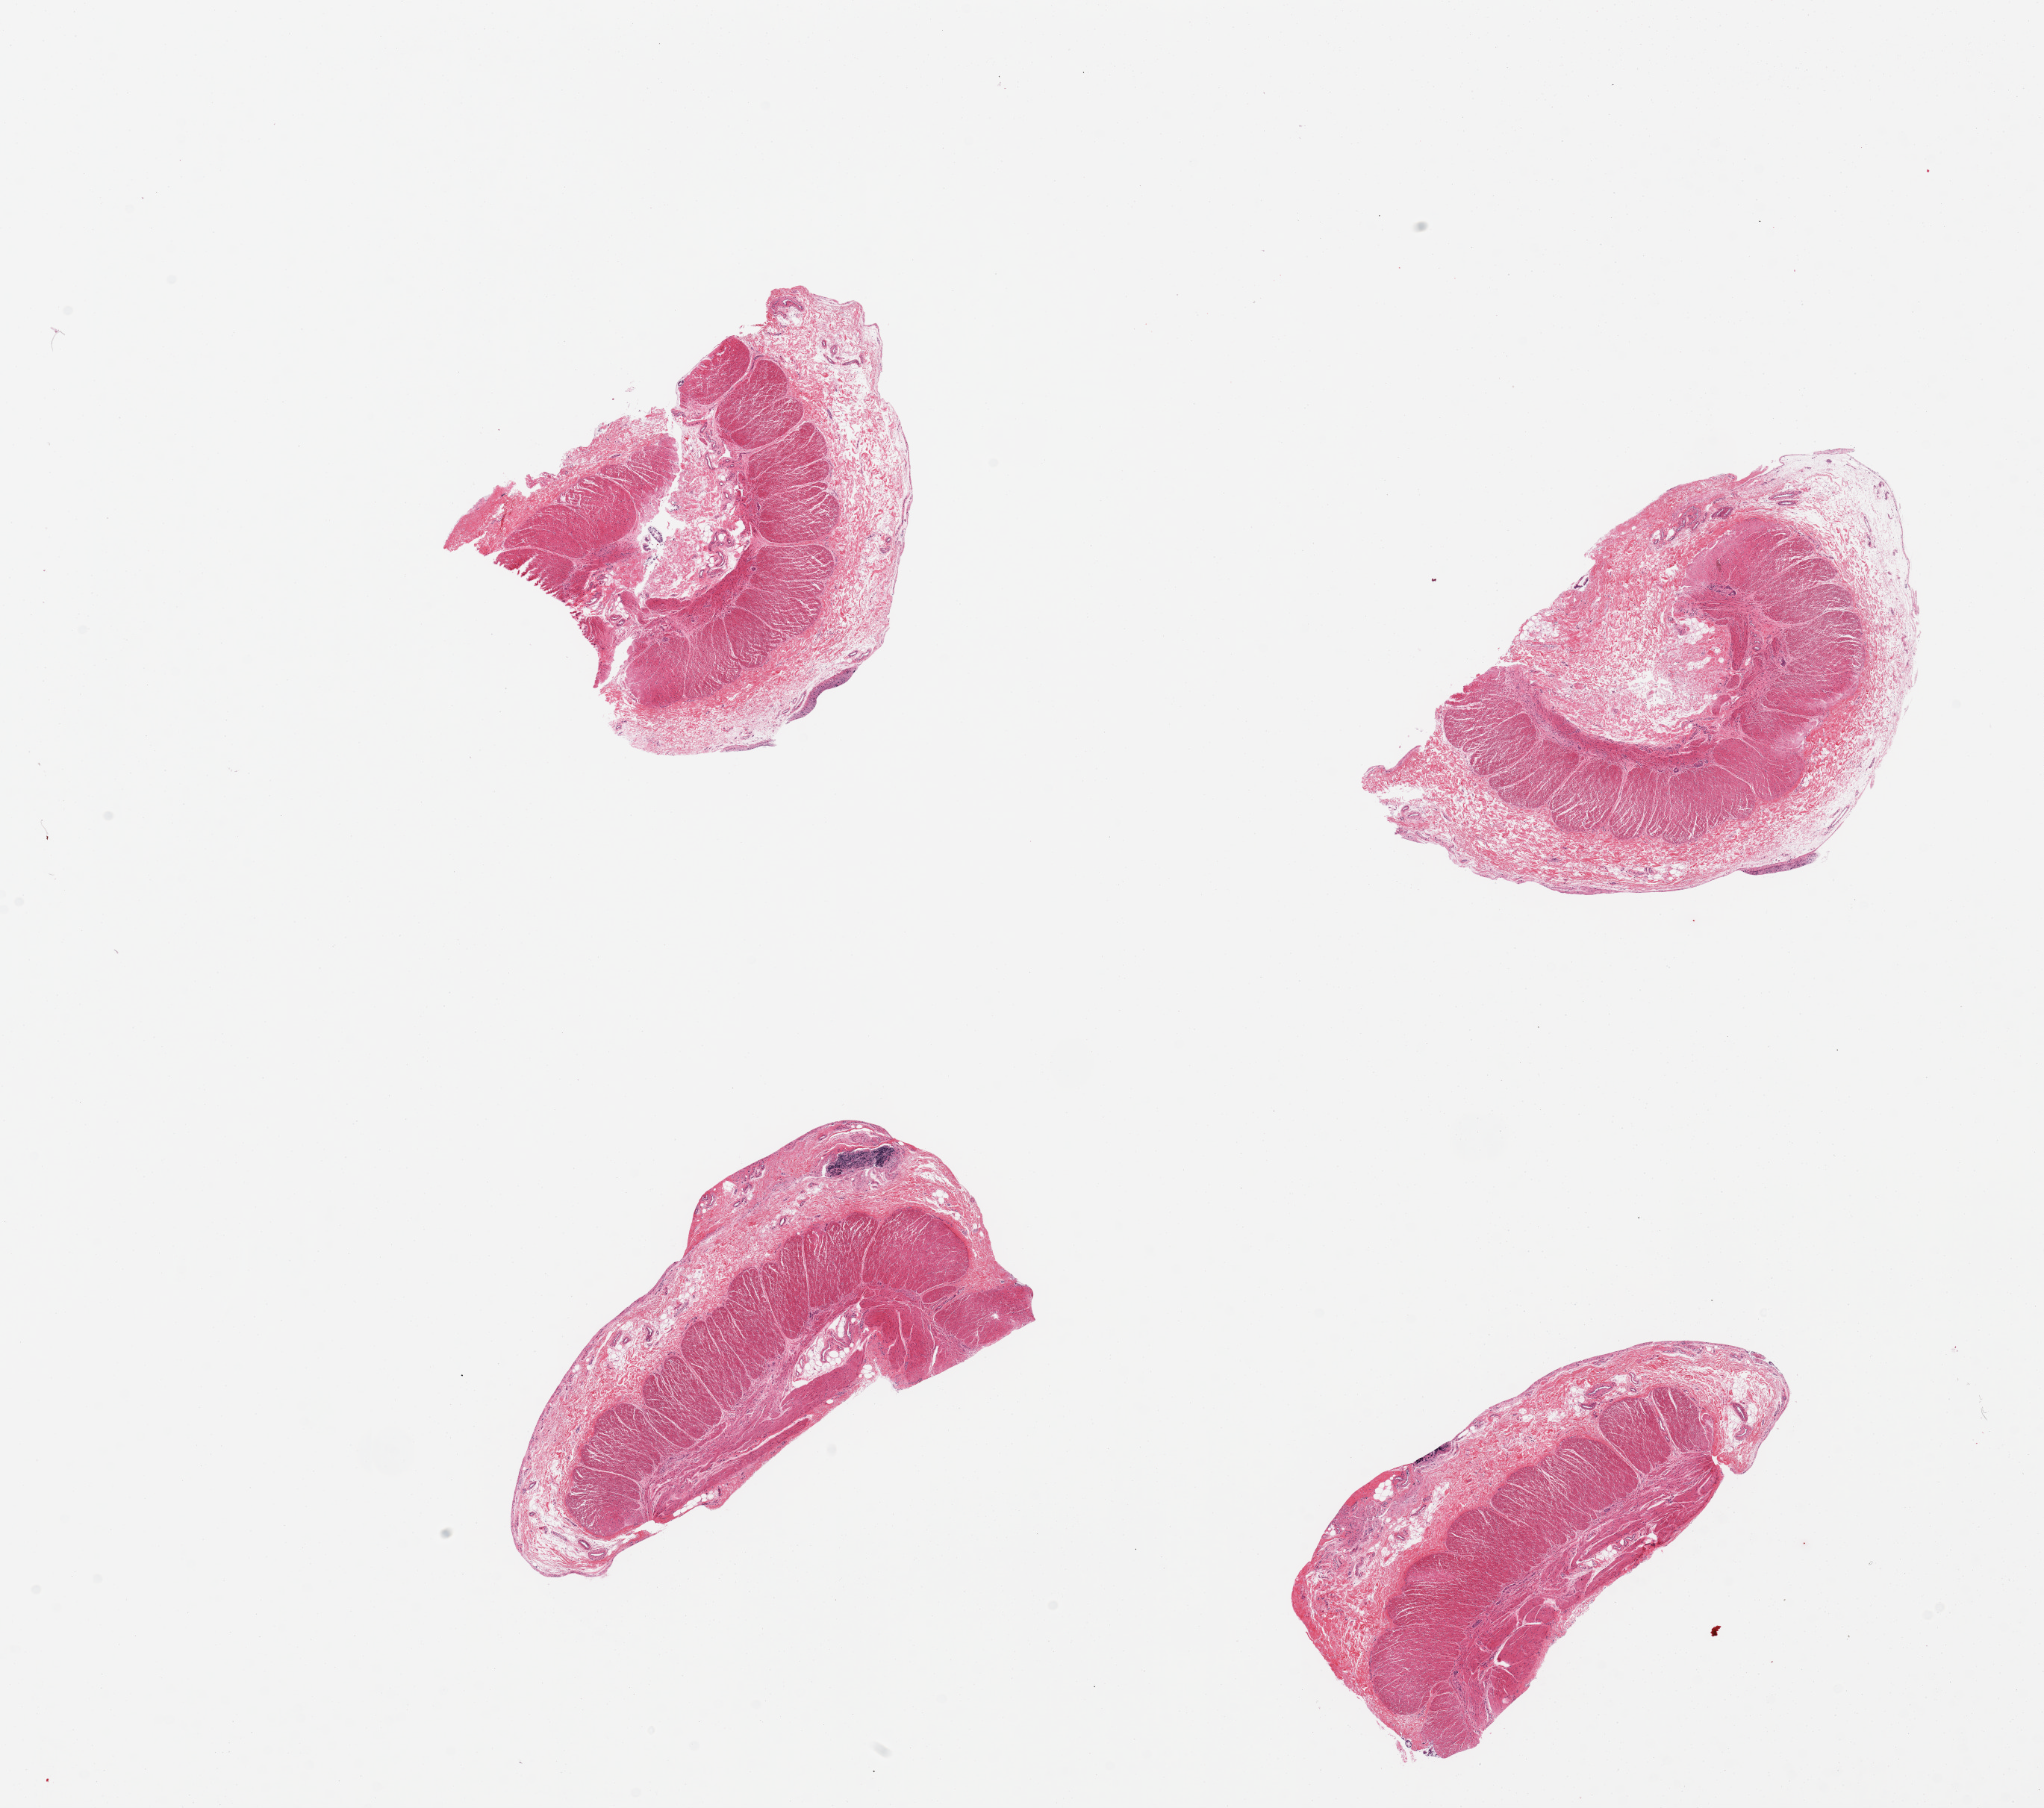
Digitized hematoxylin and eosin (H&E)-stained section — shown as a low-resolution overview of the whole scanned area (about 21.7 x 19.2 mm, slide scanned at 20x). PAXgene-fixed paraffin-embedded (PFPE) section. Sampled site (target tissue): sigmoid colon. Donor tissue sample.
Pathologist's review note for this sample: 6 pieces; submucosal edema as well as full muscularis.